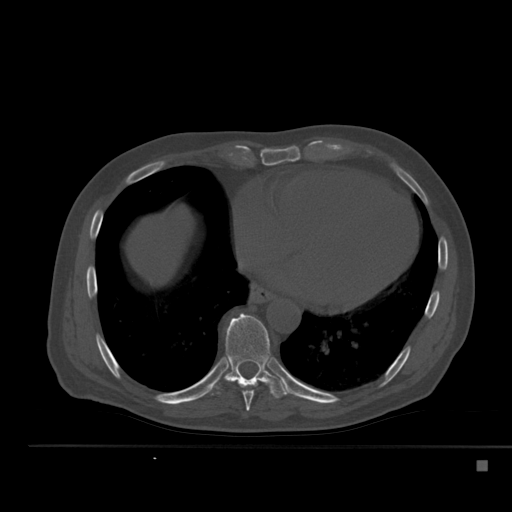
CT including the spine, one axial slice. Slice 295 of 517 in the series (ordered by position). Reconstruction kernel Br40s. 120 kVp. Bone window (W 1800 / L 400 HU). 1.5 mm slice thickness. 512 × 512 image matrix. Male patient, age 70 years. Case-level facts recorded for this patient, not image findings: primary cancer: renal; vertebrae with lytic lesions (as recorded): T4, T6, T10, T12, L3, L4, L5.
Structures marked on this image (semi-automatically segmented with operator editing):
- T8 vertebra: bounding box (x1, y1, x2, y2) in pixels: (242, 380, 259, 411)
- T9 vertebra: (207, 314, 287, 398)